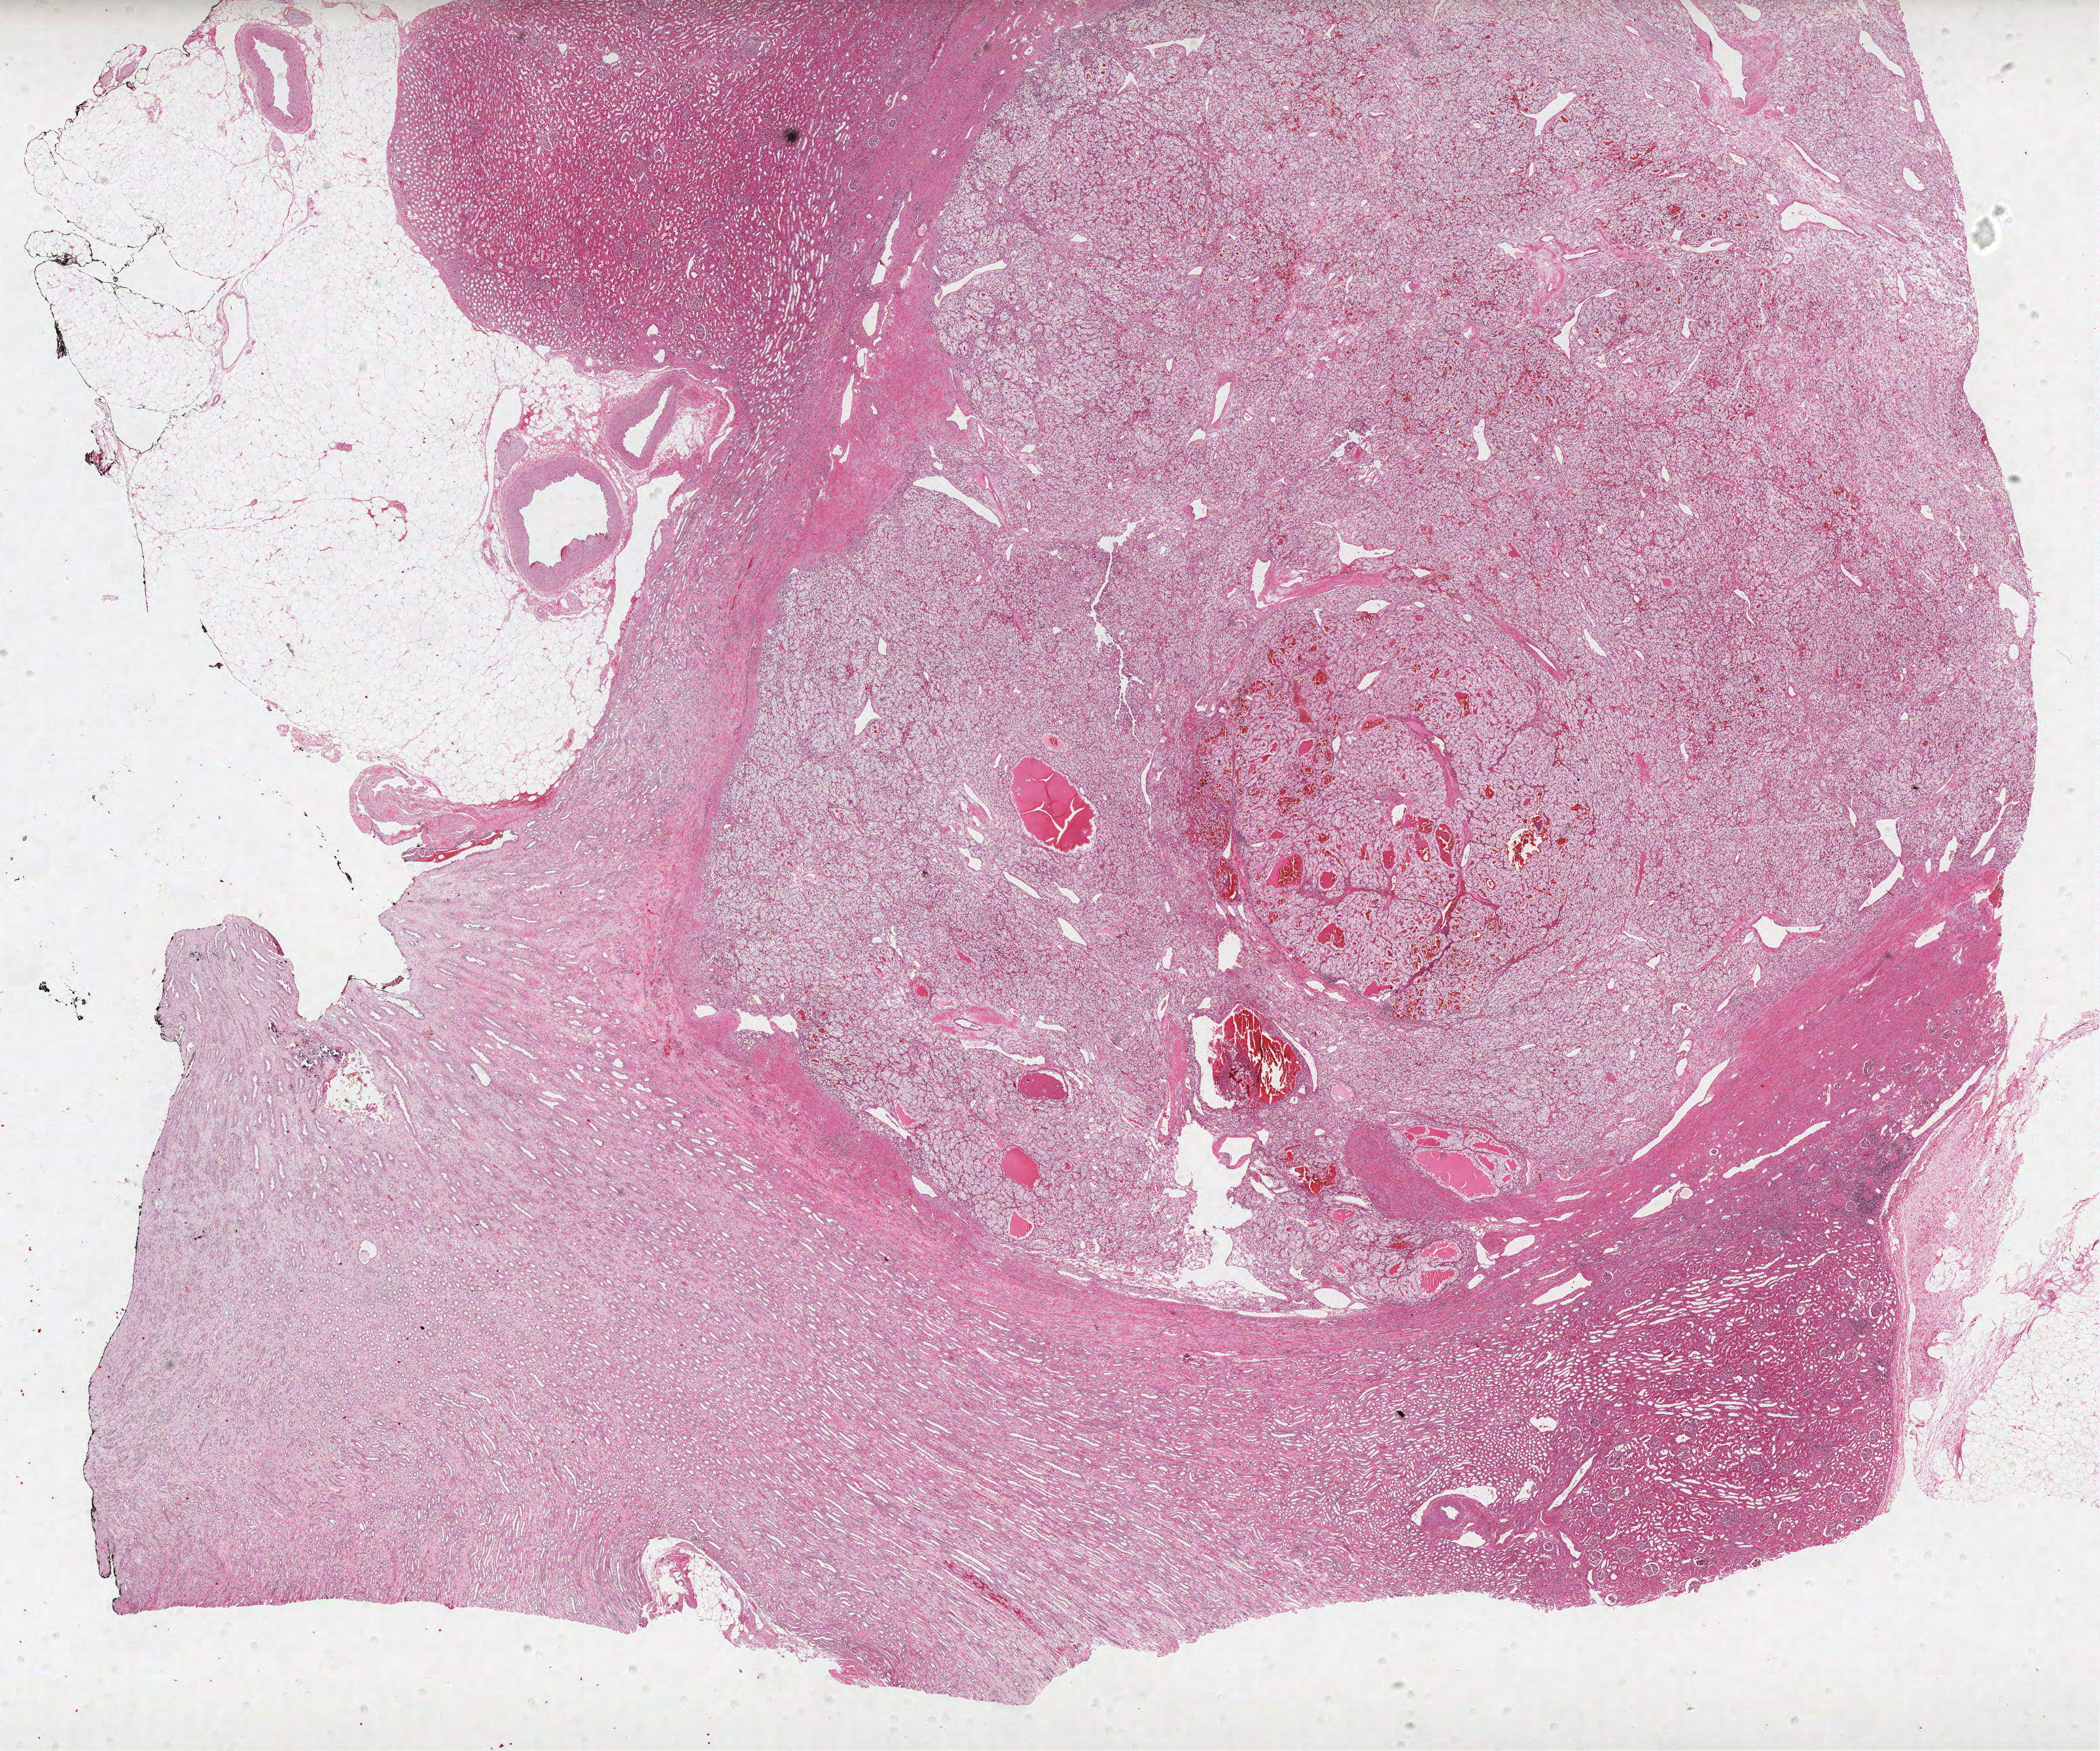
Whole-slide histology image, H&E-stained, shown as a low-resolution overview of the whole scanned area (about 25.7 x 21.4 mm, from a 40x scan); FFPE section; kidney, primary tumour sample. Patient: male, age at initial diagnosis 54 years. Histologic grade: G2 (moderately differentiated).
Laterality: right. AJCC pathologic stage: I. Histologic diagnosis: Clear cell adenocarcinoma, NOS.